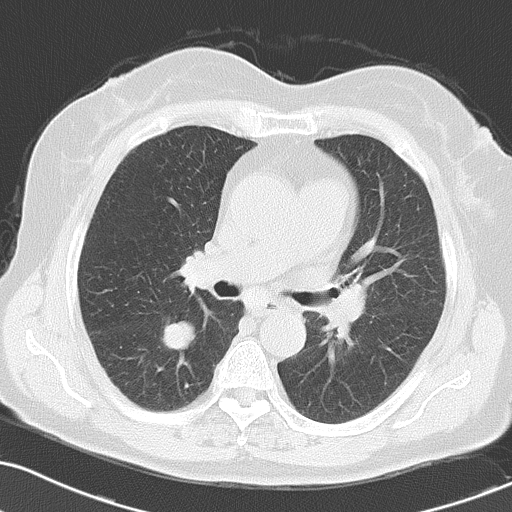
Chest CT, one axial slice. Position 34 of 55 along the scan axis. 120 kVp. Lung window (W 1500 / L -600 HU). 512 × 512 image matrix, field of view 323 × 323 mm. Female patient, age 70 years. From the clinical record (not read from this slice): clinical TNM (as recorded): T1c N3 M0; histopathological grade: G3.
Annotated regions visible in this slice (rectangle marked by the reading radiologist):
- lung tumour (recorded histology: small cell carcinoma): bounding box (x1, y1, x2, y2) in pixels: (154, 312, 211, 367)